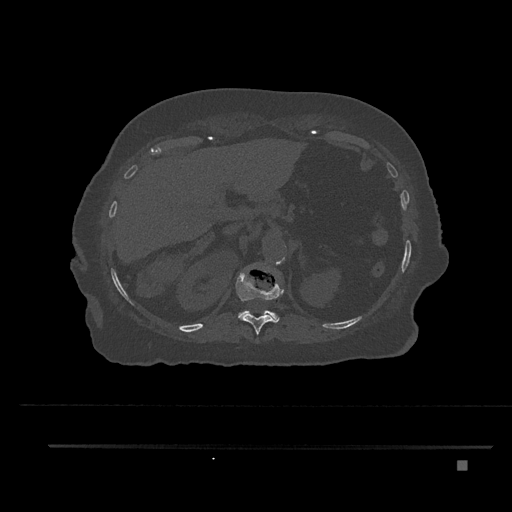
CT including the spine, one axial slice. Slice 299 of 797 in the series (ordered by position). 120 kVp. Bone window (W 1800 / L 400 HU). 0.5 mm slice thickness. 512 × 512 image matrix. Patient: female, 76 years. From the clinical record (not read from this slice): primary cancer: lung; vertebrae with lytic lesions (as recorded): T11, L3.
Outlined on this slice (semi-automatically segmented with operator editing):
- T11 vertebra: bounding box <236,268,284,335> (left, top, right, bottom; pixels)
- T12 vertebra: <238,310,279,321>